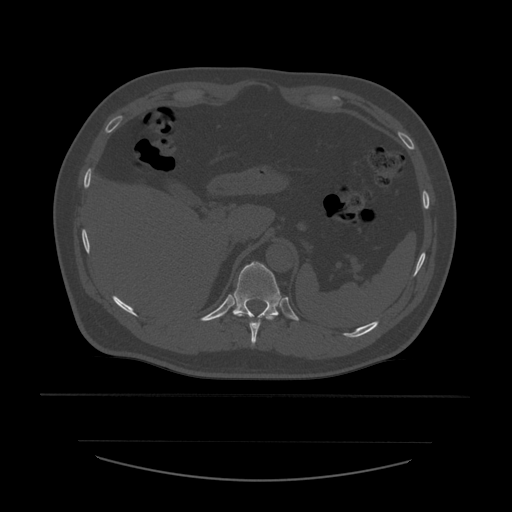
CT including the spine, one axial slice. Slice 283 of 532 in the series (ordered by position). Reconstruction kernel STANDARD. Bone window (W 1800 / L 400 HU). 512 × 512 image matrix, field of view 441 × 441 mm. Patient age 44 years. From the clinical record (not read from this slice): primary cancer: soft tissue sarcoma.
Structures marked on this image (semi-automatic segmentation, software-assisted and operator-edited):
- T10 vertebra: box from (x=238, y=315) to (x=276, y=345) px
- T11 vertebra: (x=233, y=262)–(x=282, y=319)